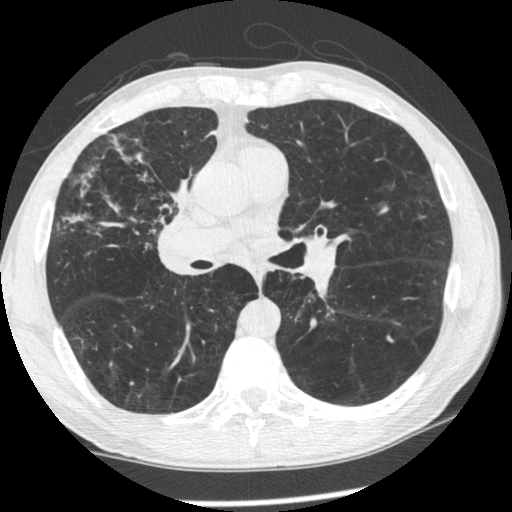
Low-dose screening chest CT, one axial slice. Position 127 of 261 along the scan axis. Reconstruction kernel STANDARD. 120 kVp. Lung window (W 1500 / L -600 HU). 1.25 mm slice thickness. 512 × 512 image matrix, field of view 340 × 340 mm.
Annotated regions visible in this slice (expert manual segmentation):
- lesion 1 (tumor, upper lobe of right lung): box from (x=172, y=176) to (x=192, y=206) px